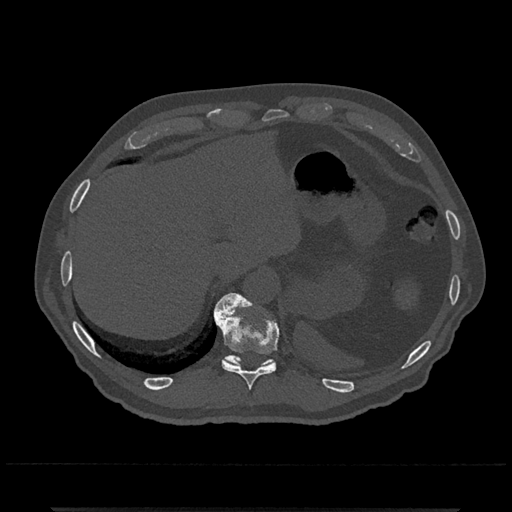
CT including the spine, one axial slice; position 538 of 797 along the scan axis; bone window (W 1800 / L 400 HU); 512 × 512 image matrix, field of view 393 × 393 mm. Patient: male, 67 years. Case-level facts recorded for this patient, not image findings: primary cancer: prostate.
Structures marked on this image (semi-automatically segmented with operator editing):
- T10 vertebra: bounding box <214,293,279,390> (left, top, right, bottom; pixels)
- T11 vertebra: <214,295,275,367>